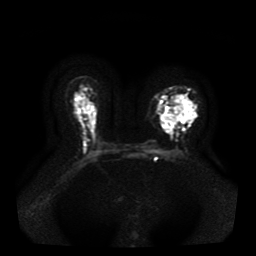
Breast MRI, one axial slice. Position 25 of 41 along the scan axis. Diffusion-weighted series; image 2 of 4 stored at this slice position (different b-values; order by instance number). 1.5 T. 5 mm slice thickness. 256 × 256 image matrix, field of view 330 × 330 mm. Female patient.
Structures marked on this image (outlined manually by an expert reader):
- tumour on diffusion-weighted imaging: bounding box <161,96,194,133> (left, top, right, bottom; pixels)